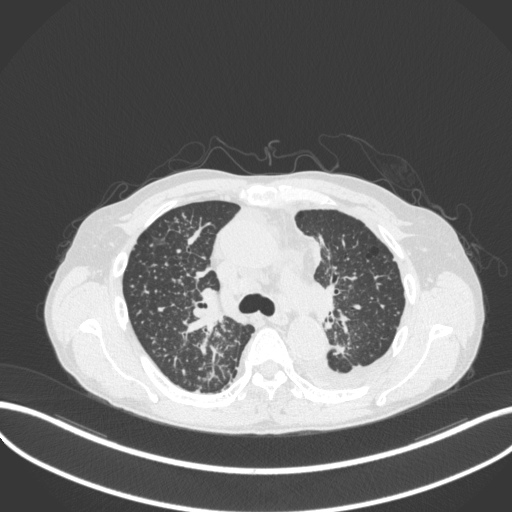
Chest CT, one axial slice; position 242 of 319 along the scan axis; reconstruction kernel B31f; lung window (W 1500 / L -600 HU); 1 mm slice thickness; 512 × 512 image matrix. Patient: male, 58 years. Case-level facts recorded for this patient, not image findings: clinical TNM (as recorded): T1c N3 M1.
Structures marked on this image (bounding box drawn by a radiologist):
- lung tumour (recorded histology: adenocarcinoma): bounding box [x1, y1, x2, y2] px = [330, 338, 349, 358]